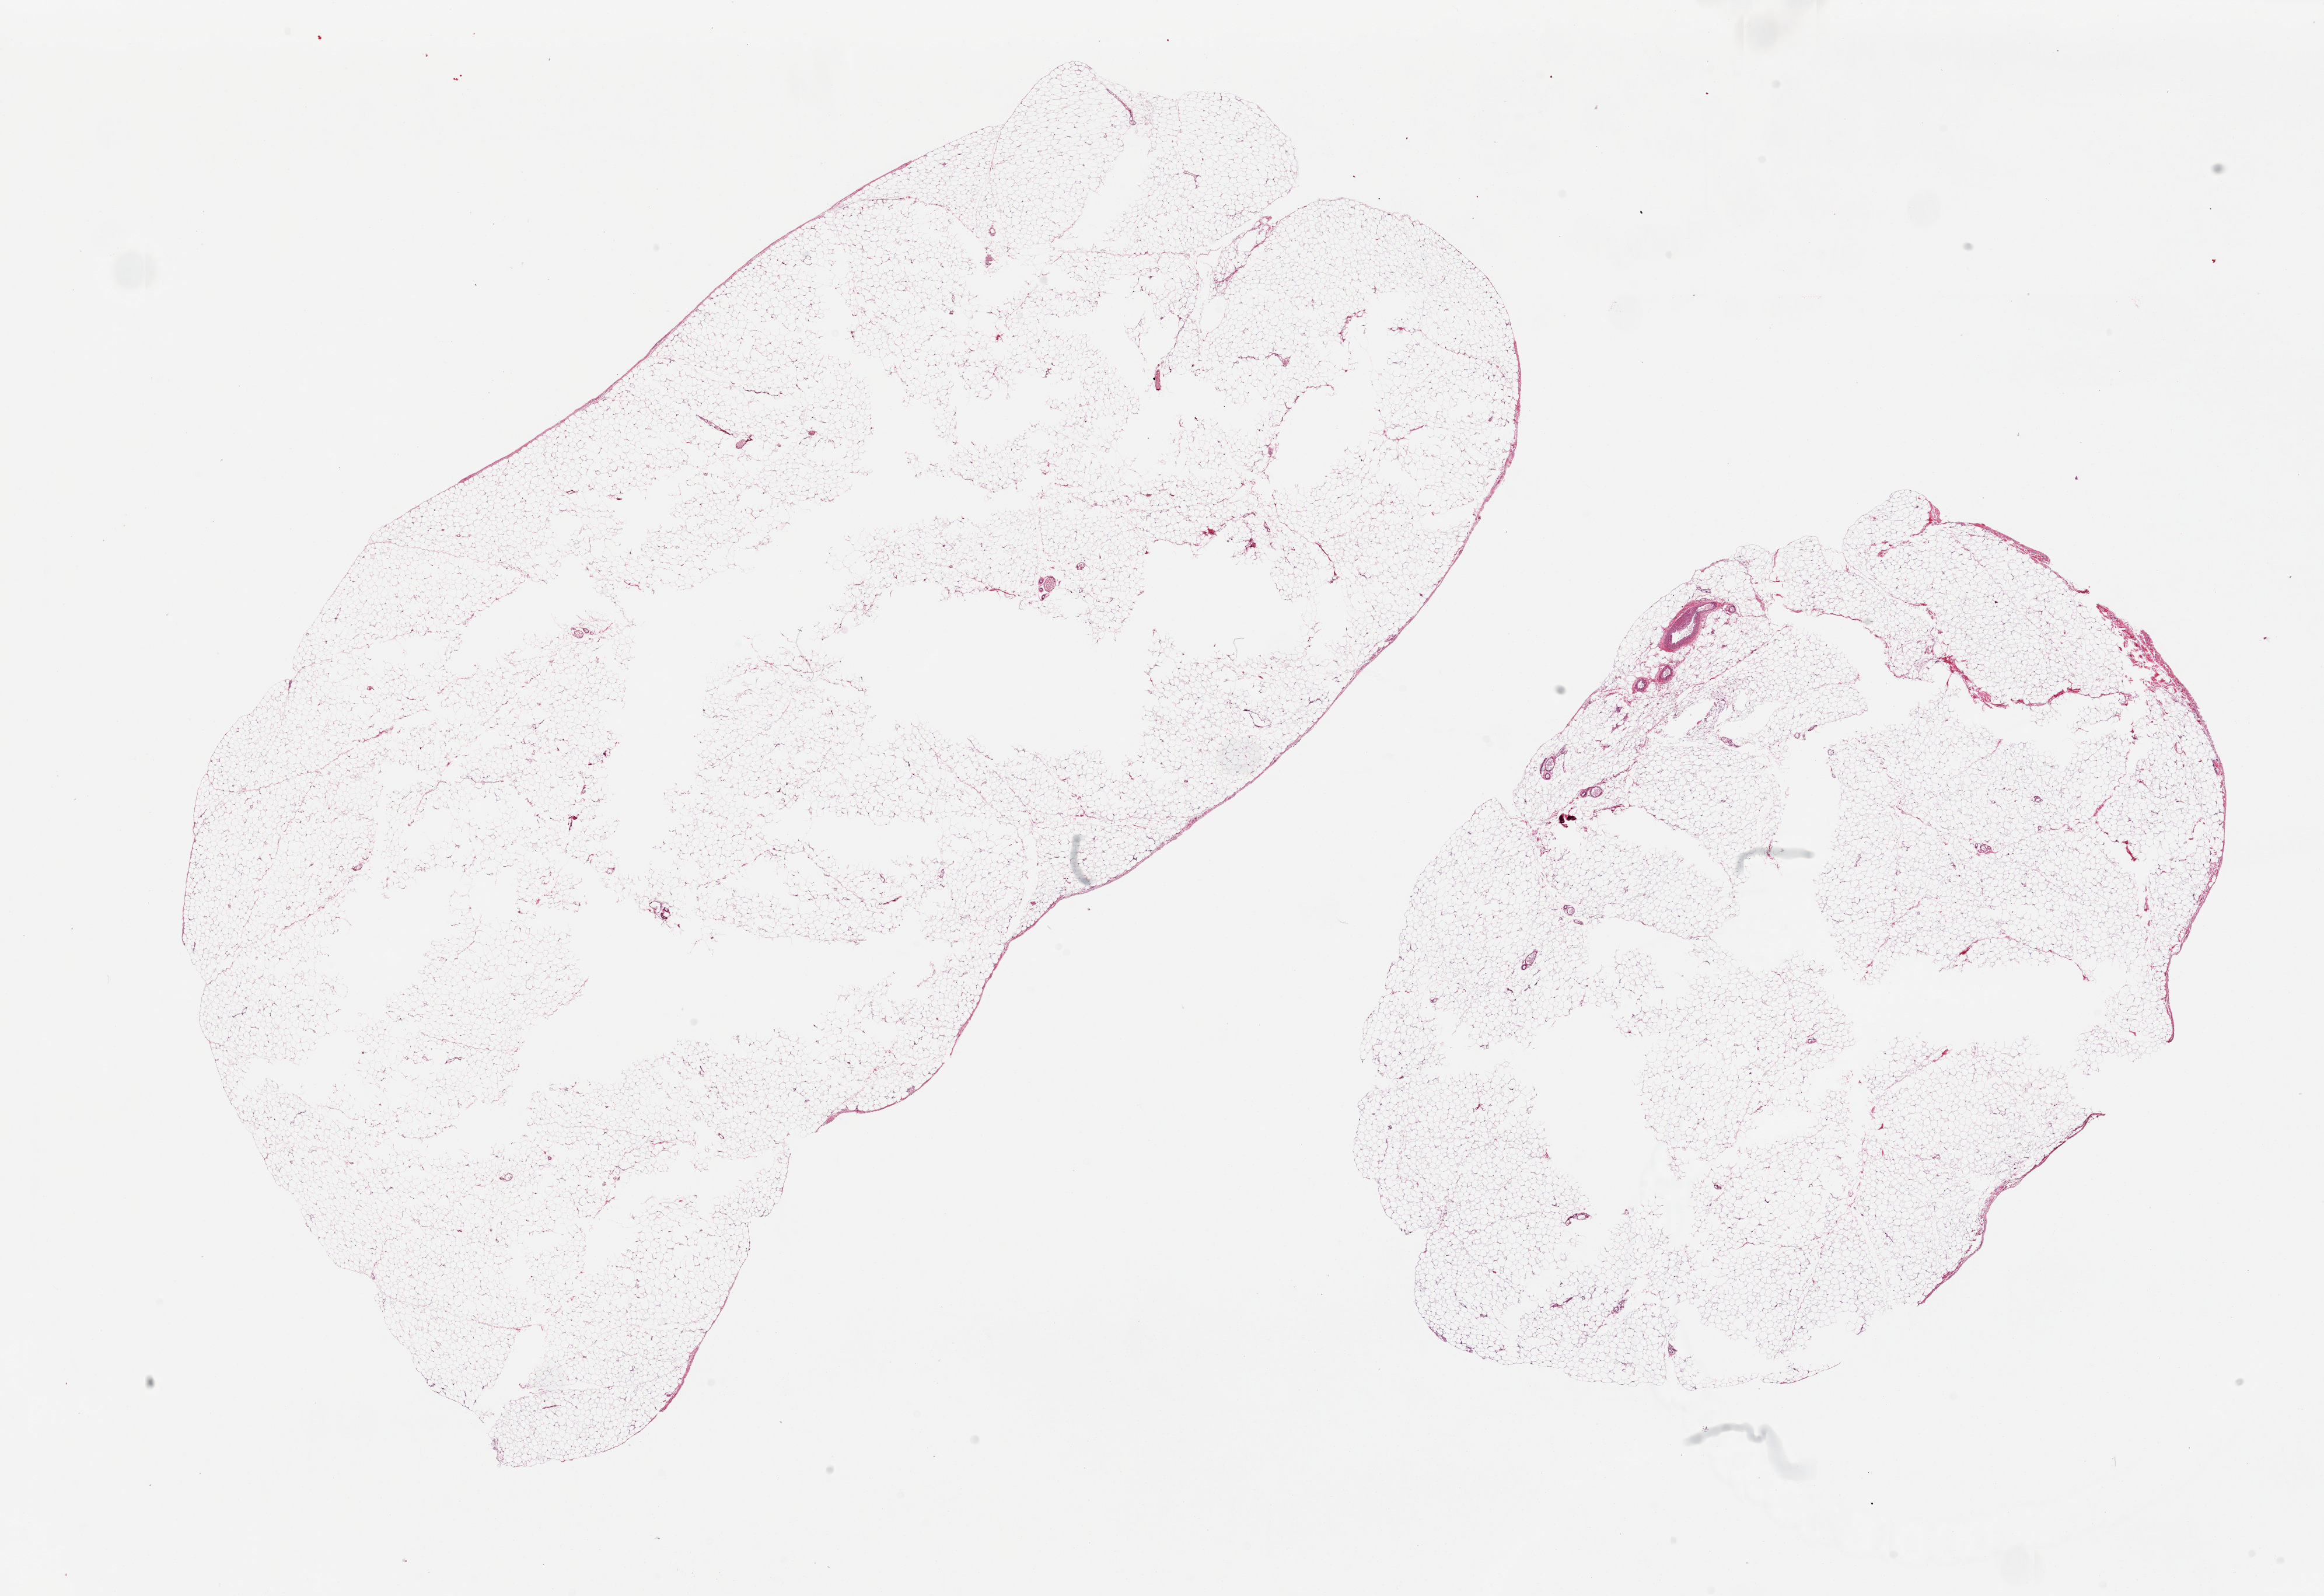
H&E whole-slide image — whole scanned area (about 31.5 x 21.6 mm) shown as a low-resolution overview; PAXgene-fixed, paraffin-embedded tissue; target tissue: omentum; tissue donor sample. Donor sex: female.
• reviewer comment on this tissue sample: 2 pieces. Overly large specimens with central hollow defects